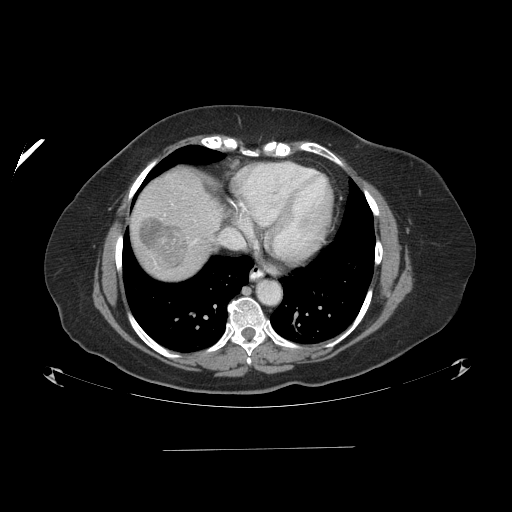
Contrast-enhanced abdominal CT (liver protocol), one axial slice; slice 81 of 103 in the series (ordered by position); reconstruction kernel STANDARD; one of 2 acquisitions stored at this slice position; soft-tissue window (W 400 / L 40 HU); 2.5 mm slice thickness; 512 × 512 image matrix. Case-level facts recorded for this patient, not image findings: diagnosis: hepatocellular carcinoma (patient treated with transarterial chemoembolisation; whether this scan precedes or follows treatment is not stated here); TNM stage (as recorded): Stage-IIIA; Child-Pugh class: A; tumour differentiation: poorly differentiated; tumour nodularity: multinodular.
Annotated regions visible in this slice (semi-automatic segmentation, software-assisted and operator-edited):
- liver parenchyma outside the tumour (the mass and vessels are separate outlines, so this box may not span the whole liver): box from (x=130, y=168) to (x=222, y=280) px
- mass: (x=139, y=216)–(x=189, y=267)
- liver vessels: (x=193, y=241)–(x=196, y=243)